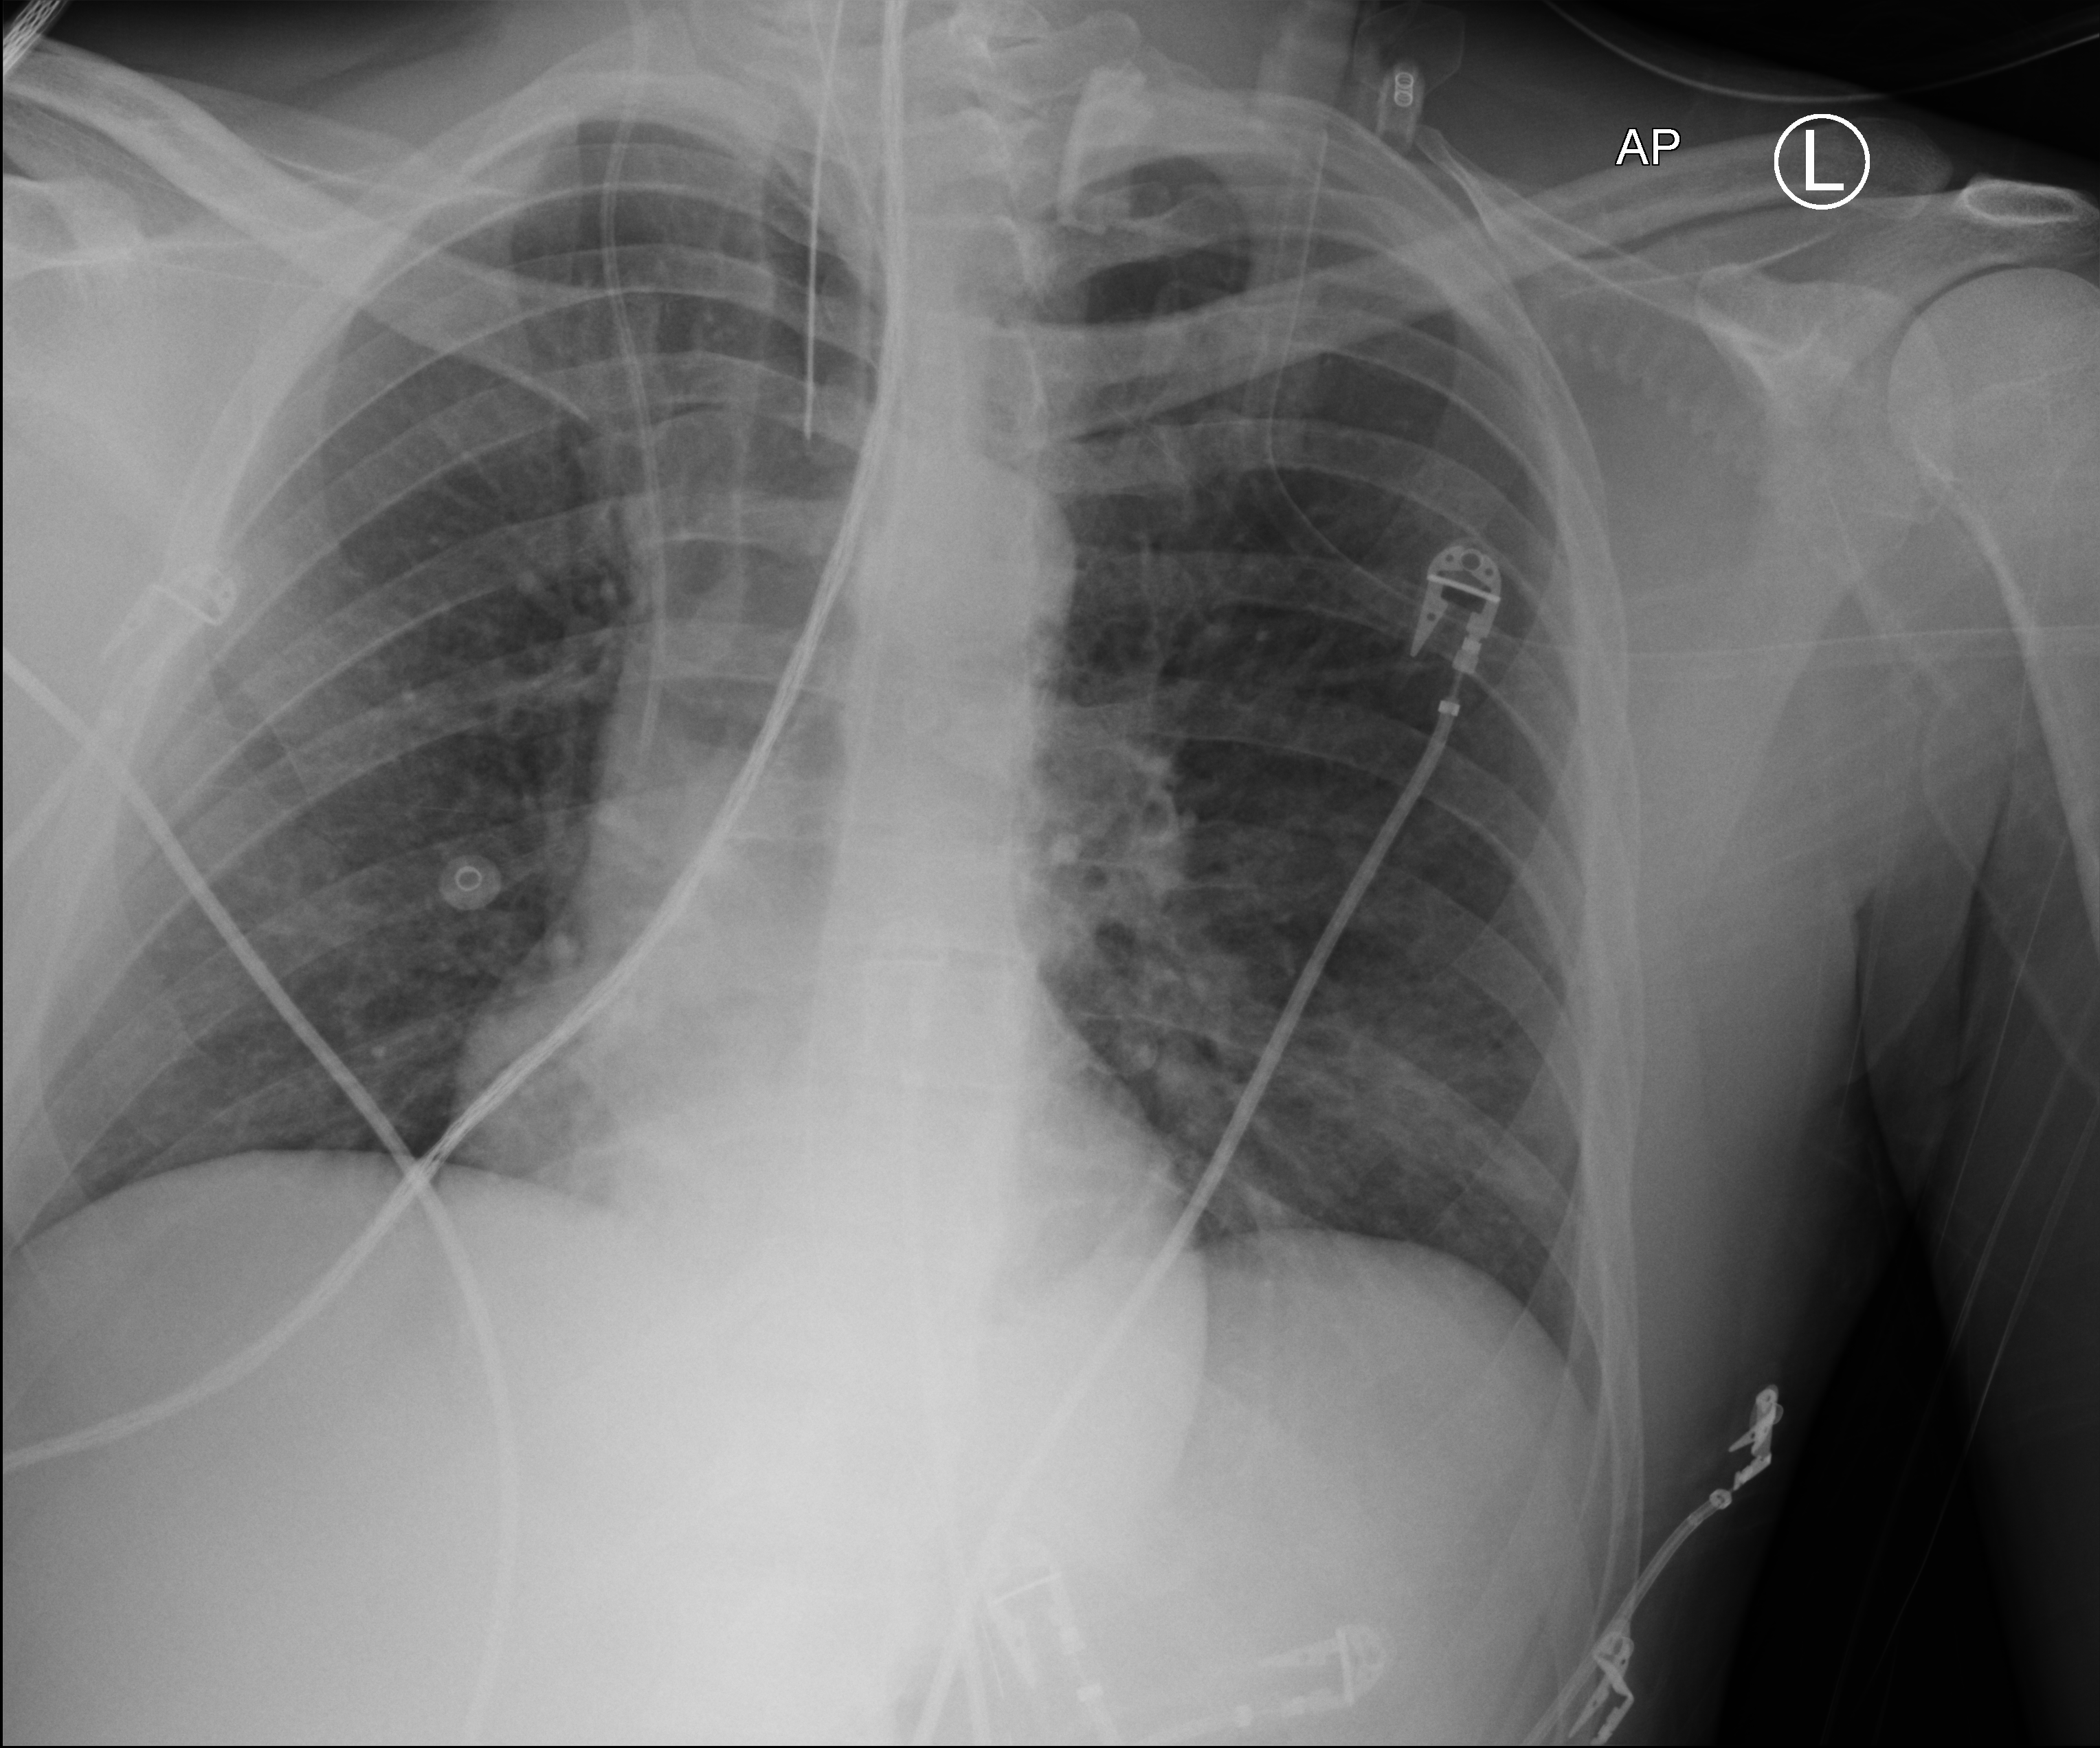
Portable chest radiograph. Patient hospitalised with COVID-19; male, aged 18–59 years.
Hospital-stay facts (about this admission, not read from this image; timing relative to this image not recorded):
- admitted to intensive care during this hospital stay: no